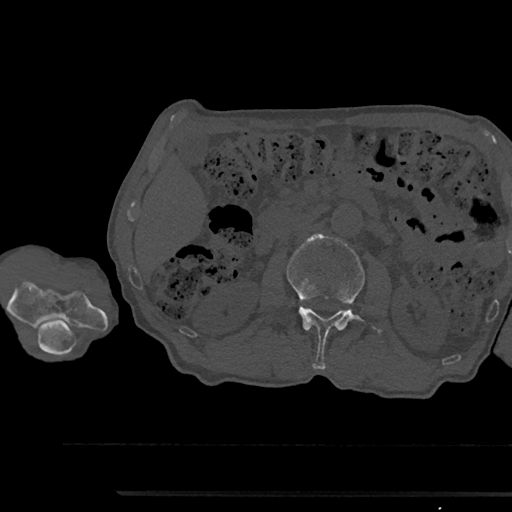
CT including the spine, one axial slice. Position 560 of 797 along the scan axis. 120 kVp. Bone window (W 1800 / L 400 HU). 0.5 mm slice thickness. 512 × 512 image matrix. Male patient, age 79 years. From the clinical record (not read from this slice): primary cancer: prostate.
Annotated regions visible in this slice (semi-automatic segmentation, software-assisted and operator-edited):
- L2 vertebra: bounding box <286,234,379,369> (left, top, right, bottom; pixels)